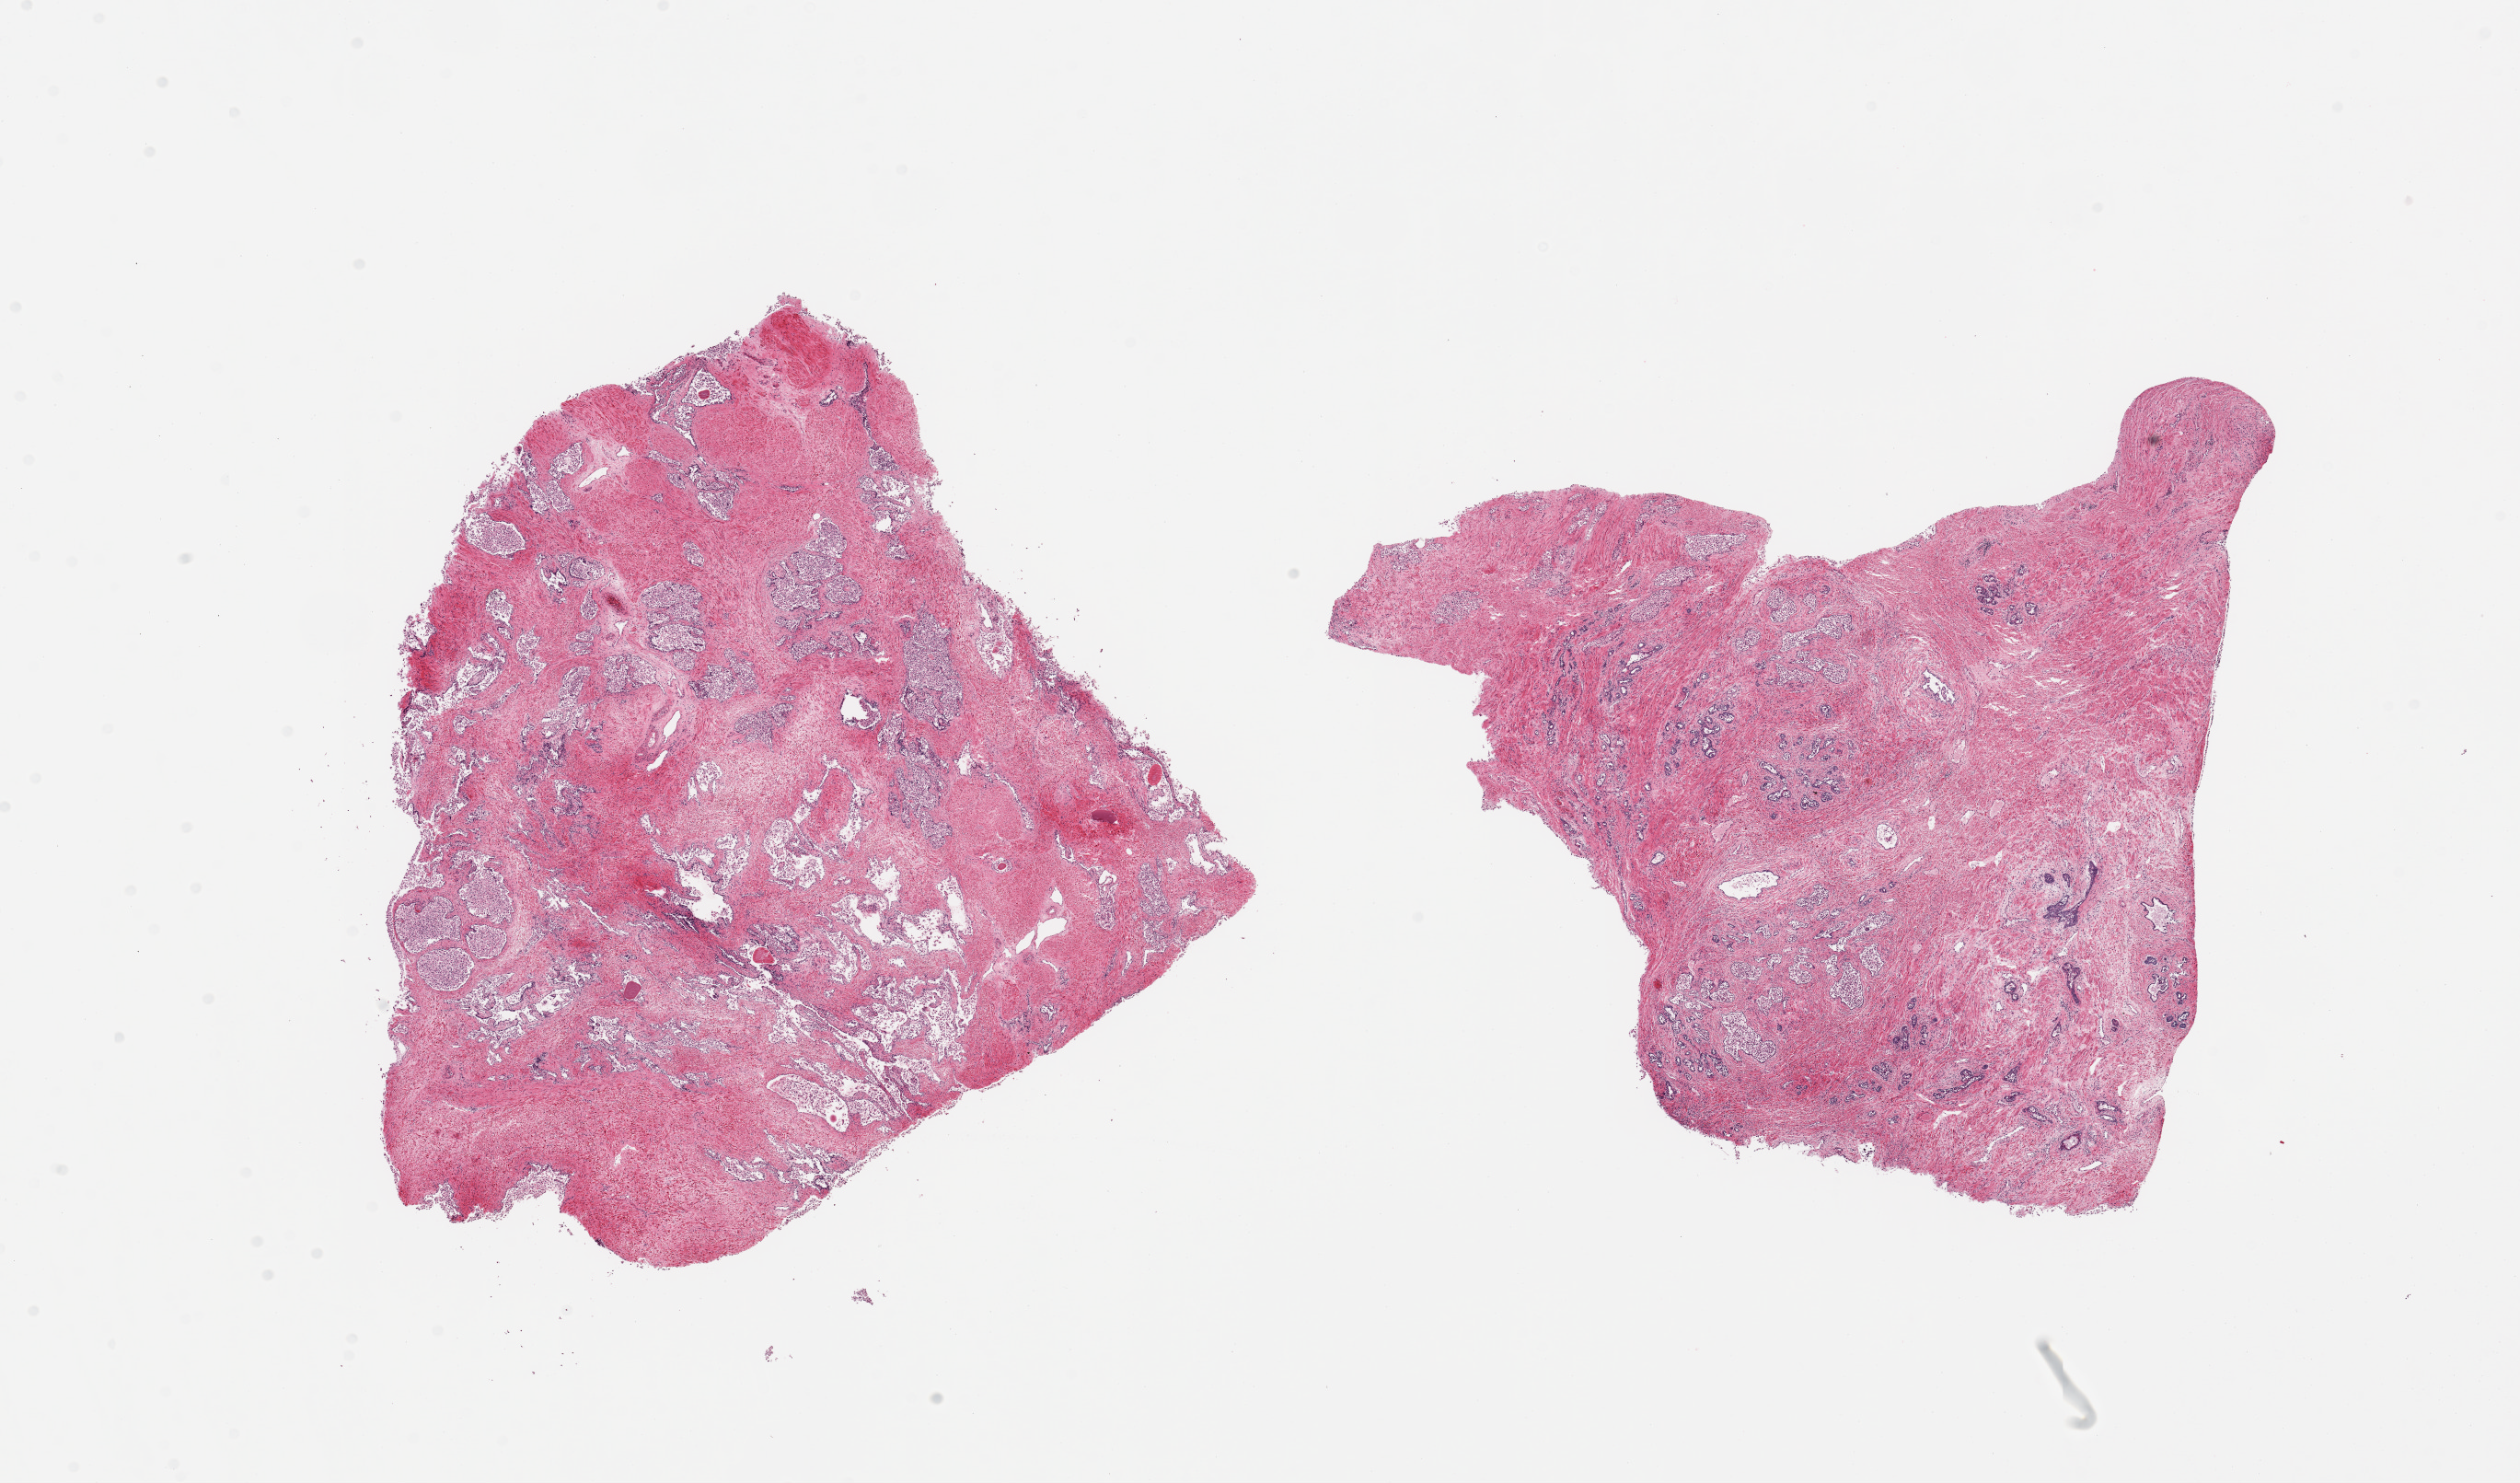
Haematoxylin and eosin whole-slide image — a low-resolution overview of the entire scanned area, about 21.7 x 12.7 mm (acquisition: 20x scan); PAXgene-fixed, paraffin-embedded tissue; section of prostate (target tissue); tissue donor sample. Donor sex: male.
Reviewer comment on this tissue sample: 2 pieces, glandular elements with advanced autolysis, apparent hyperplastic pattern.